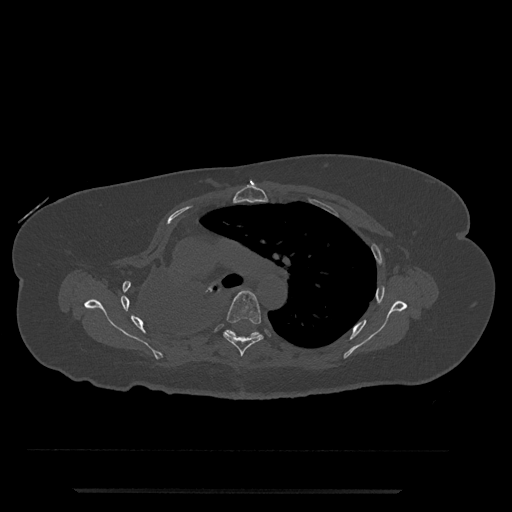
CT including the spine, one axial slice; position 535 of 797 along the scan axis; reconstruction kernel Br40s/3; 120 kVp; bone window (W 1800 / L 400 HU); 0.5 mm slice thickness; 512 × 512 image matrix, field of view 440 × 440 mm. Patient: female, 51 years. From the clinical record (not read from this slice): primary cancer: neuro; vertebrae with lytic lesions (as recorded): T8.
Annotated regions visible in this slice (semi-automatic segmentation, software-assisted and operator-edited):
- T5 vertebra: box from (x=223, y=290) to (x=264, y=357) px
- T6 vertebra: (x=225, y=330)–(x=260, y=338)